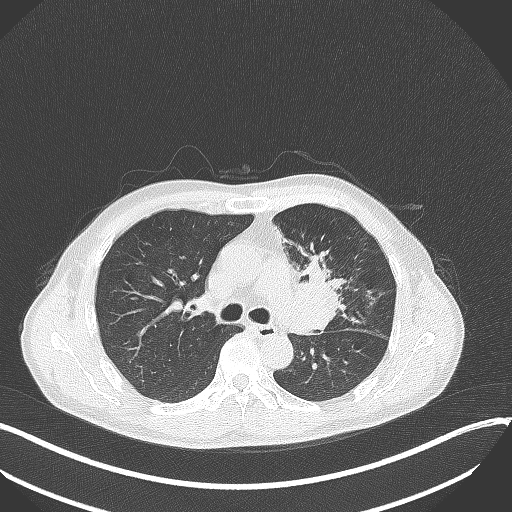
Chest CT, one axial slice; slice 214 of 411 in the series (ordered by position); lung window (W 1500 / L -600 HU); 1 mm slice thickness; 512 × 512 image matrix, field of view 400 × 400 mm. Male patient, age 56 years. Case-level facts recorded for this patient, not image findings: clinical TNM (as recorded): T2a N0 M0.
Annotated regions visible in this slice (bounding box drawn by a radiologist):
- lung tumour (recorded histology: squamous cell carcinoma): bounding box <290,248,347,341> (left, top, right, bottom; pixels)